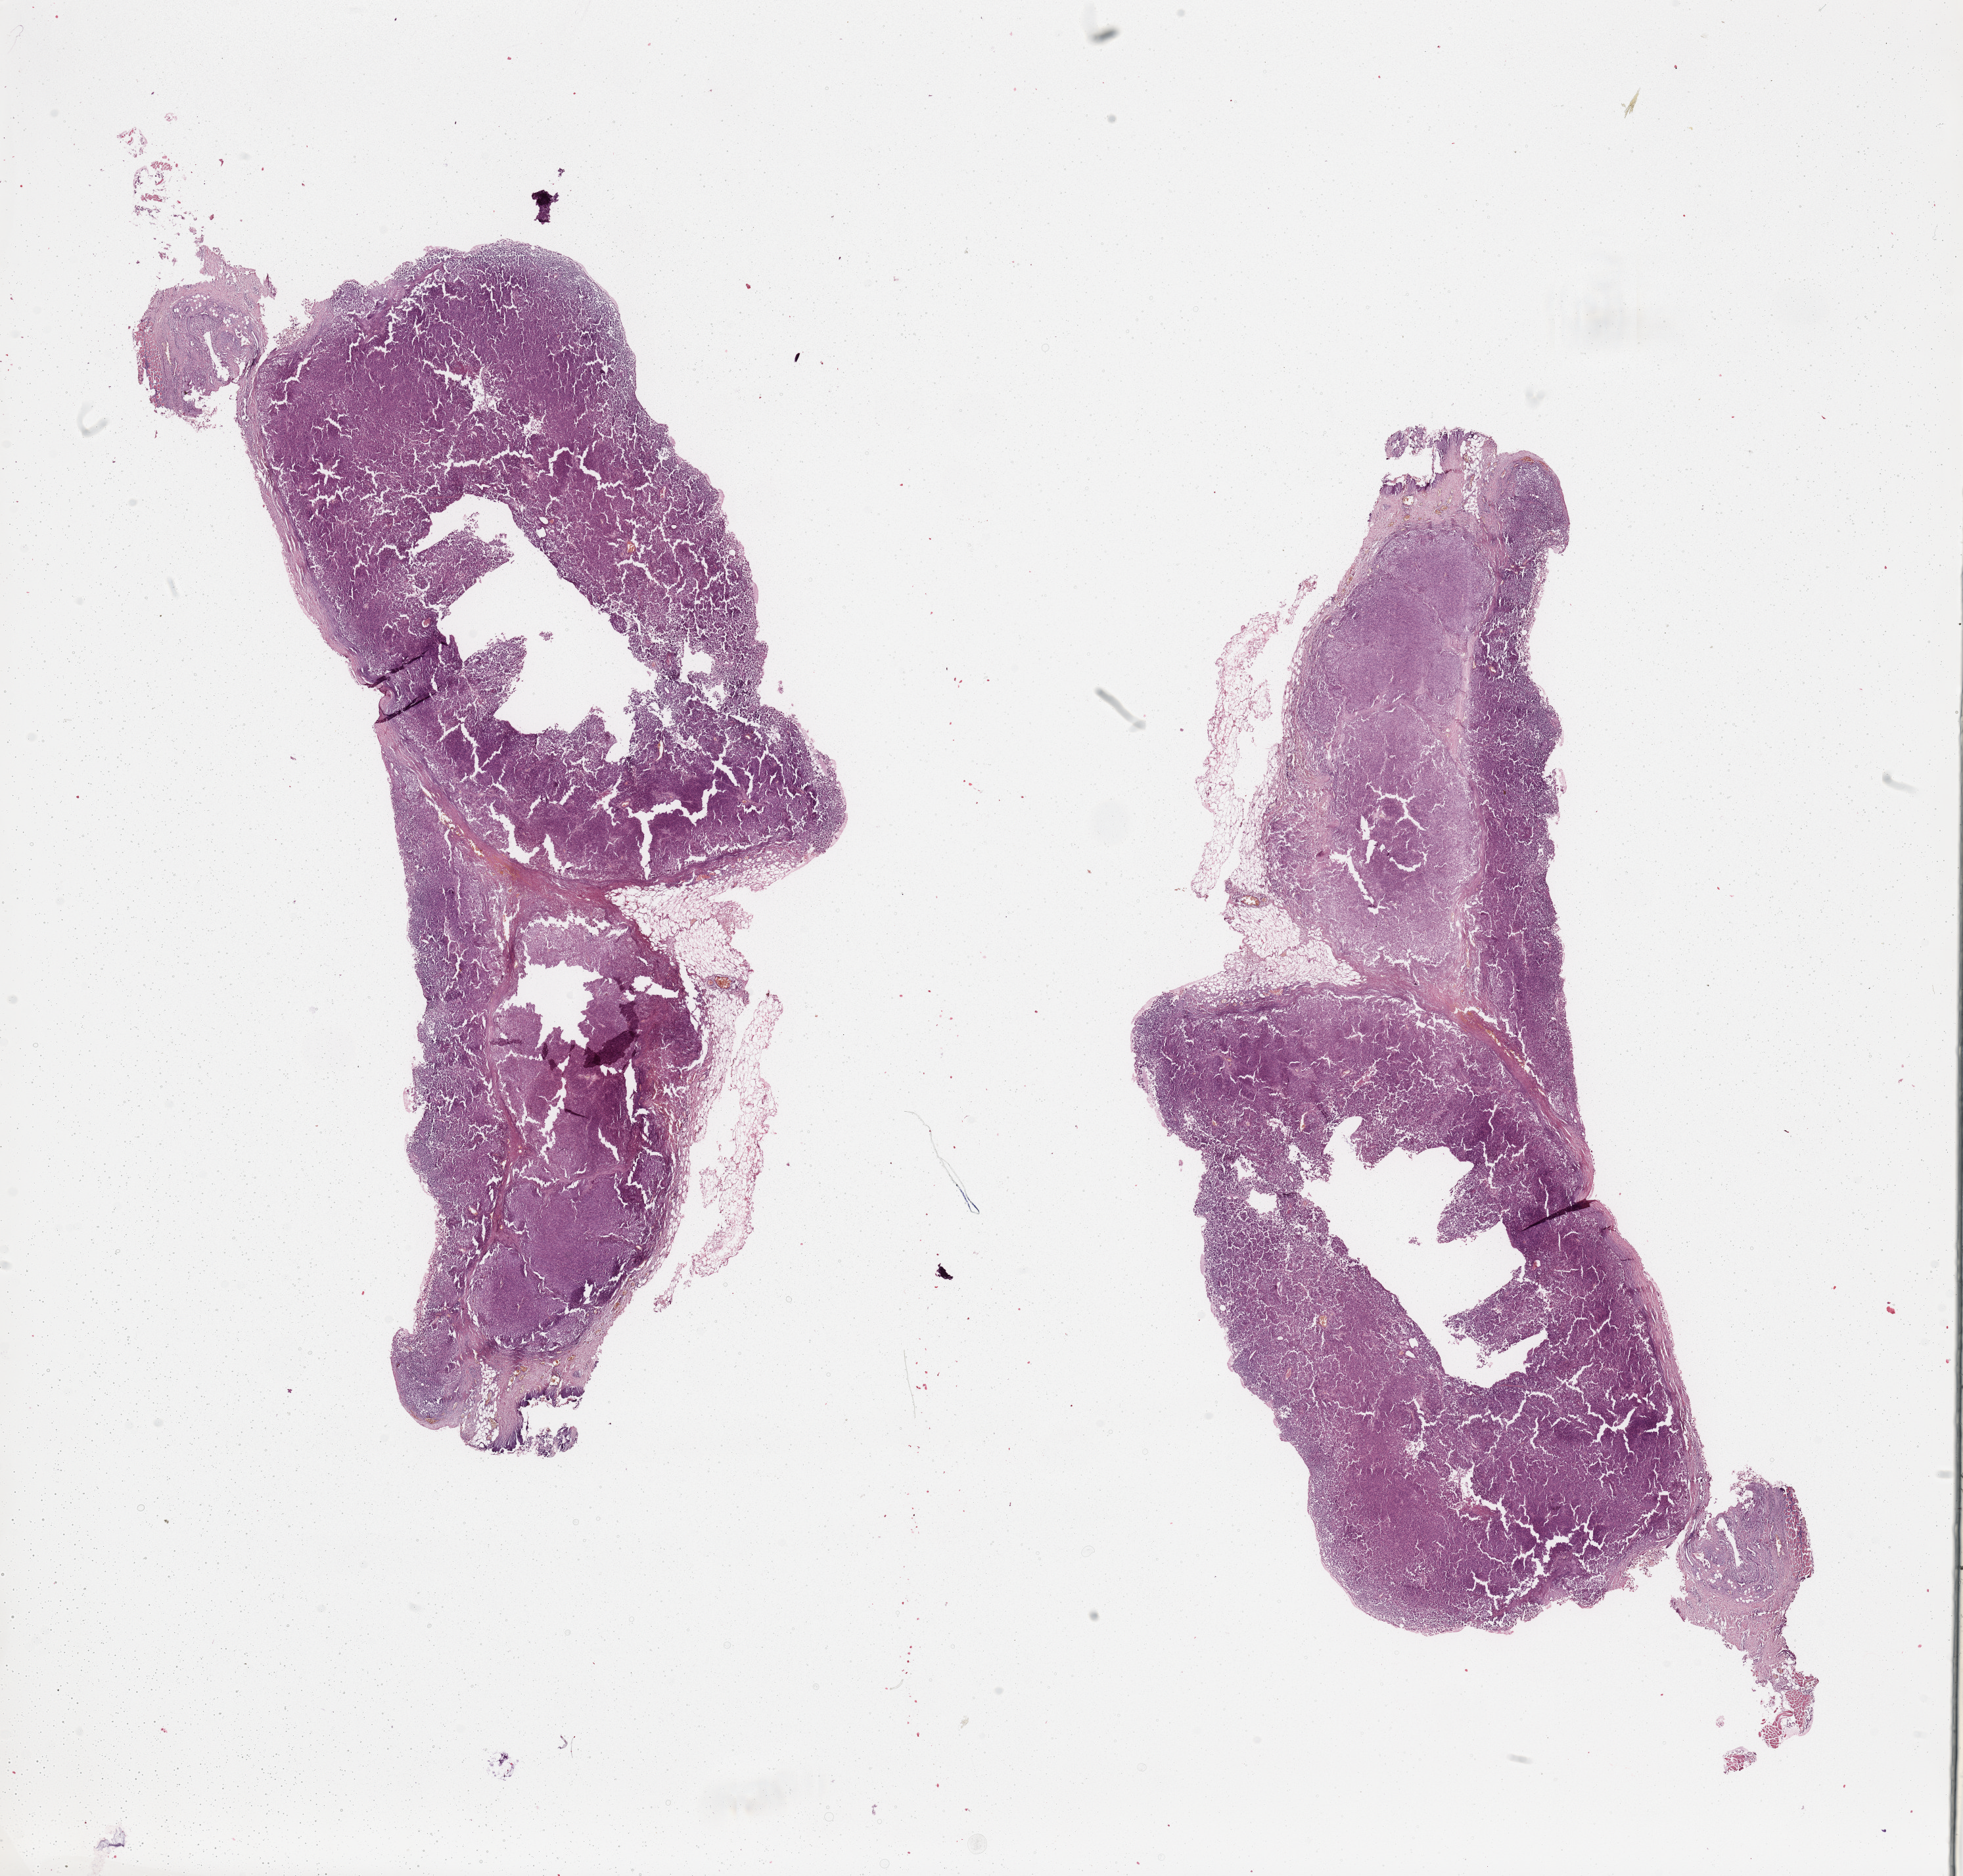
Whole-slide histology image, H&E, shown as a low-resolution overview of the whole scanned area (about 23.6 x 22.6 mm, from a 20x scan), melanoma tumour tissue; sampled site not recorded. 45-year-old female patient.
• diagnosis: Malignant melanoma, NOS
• AJCC pathologic stage: IIA